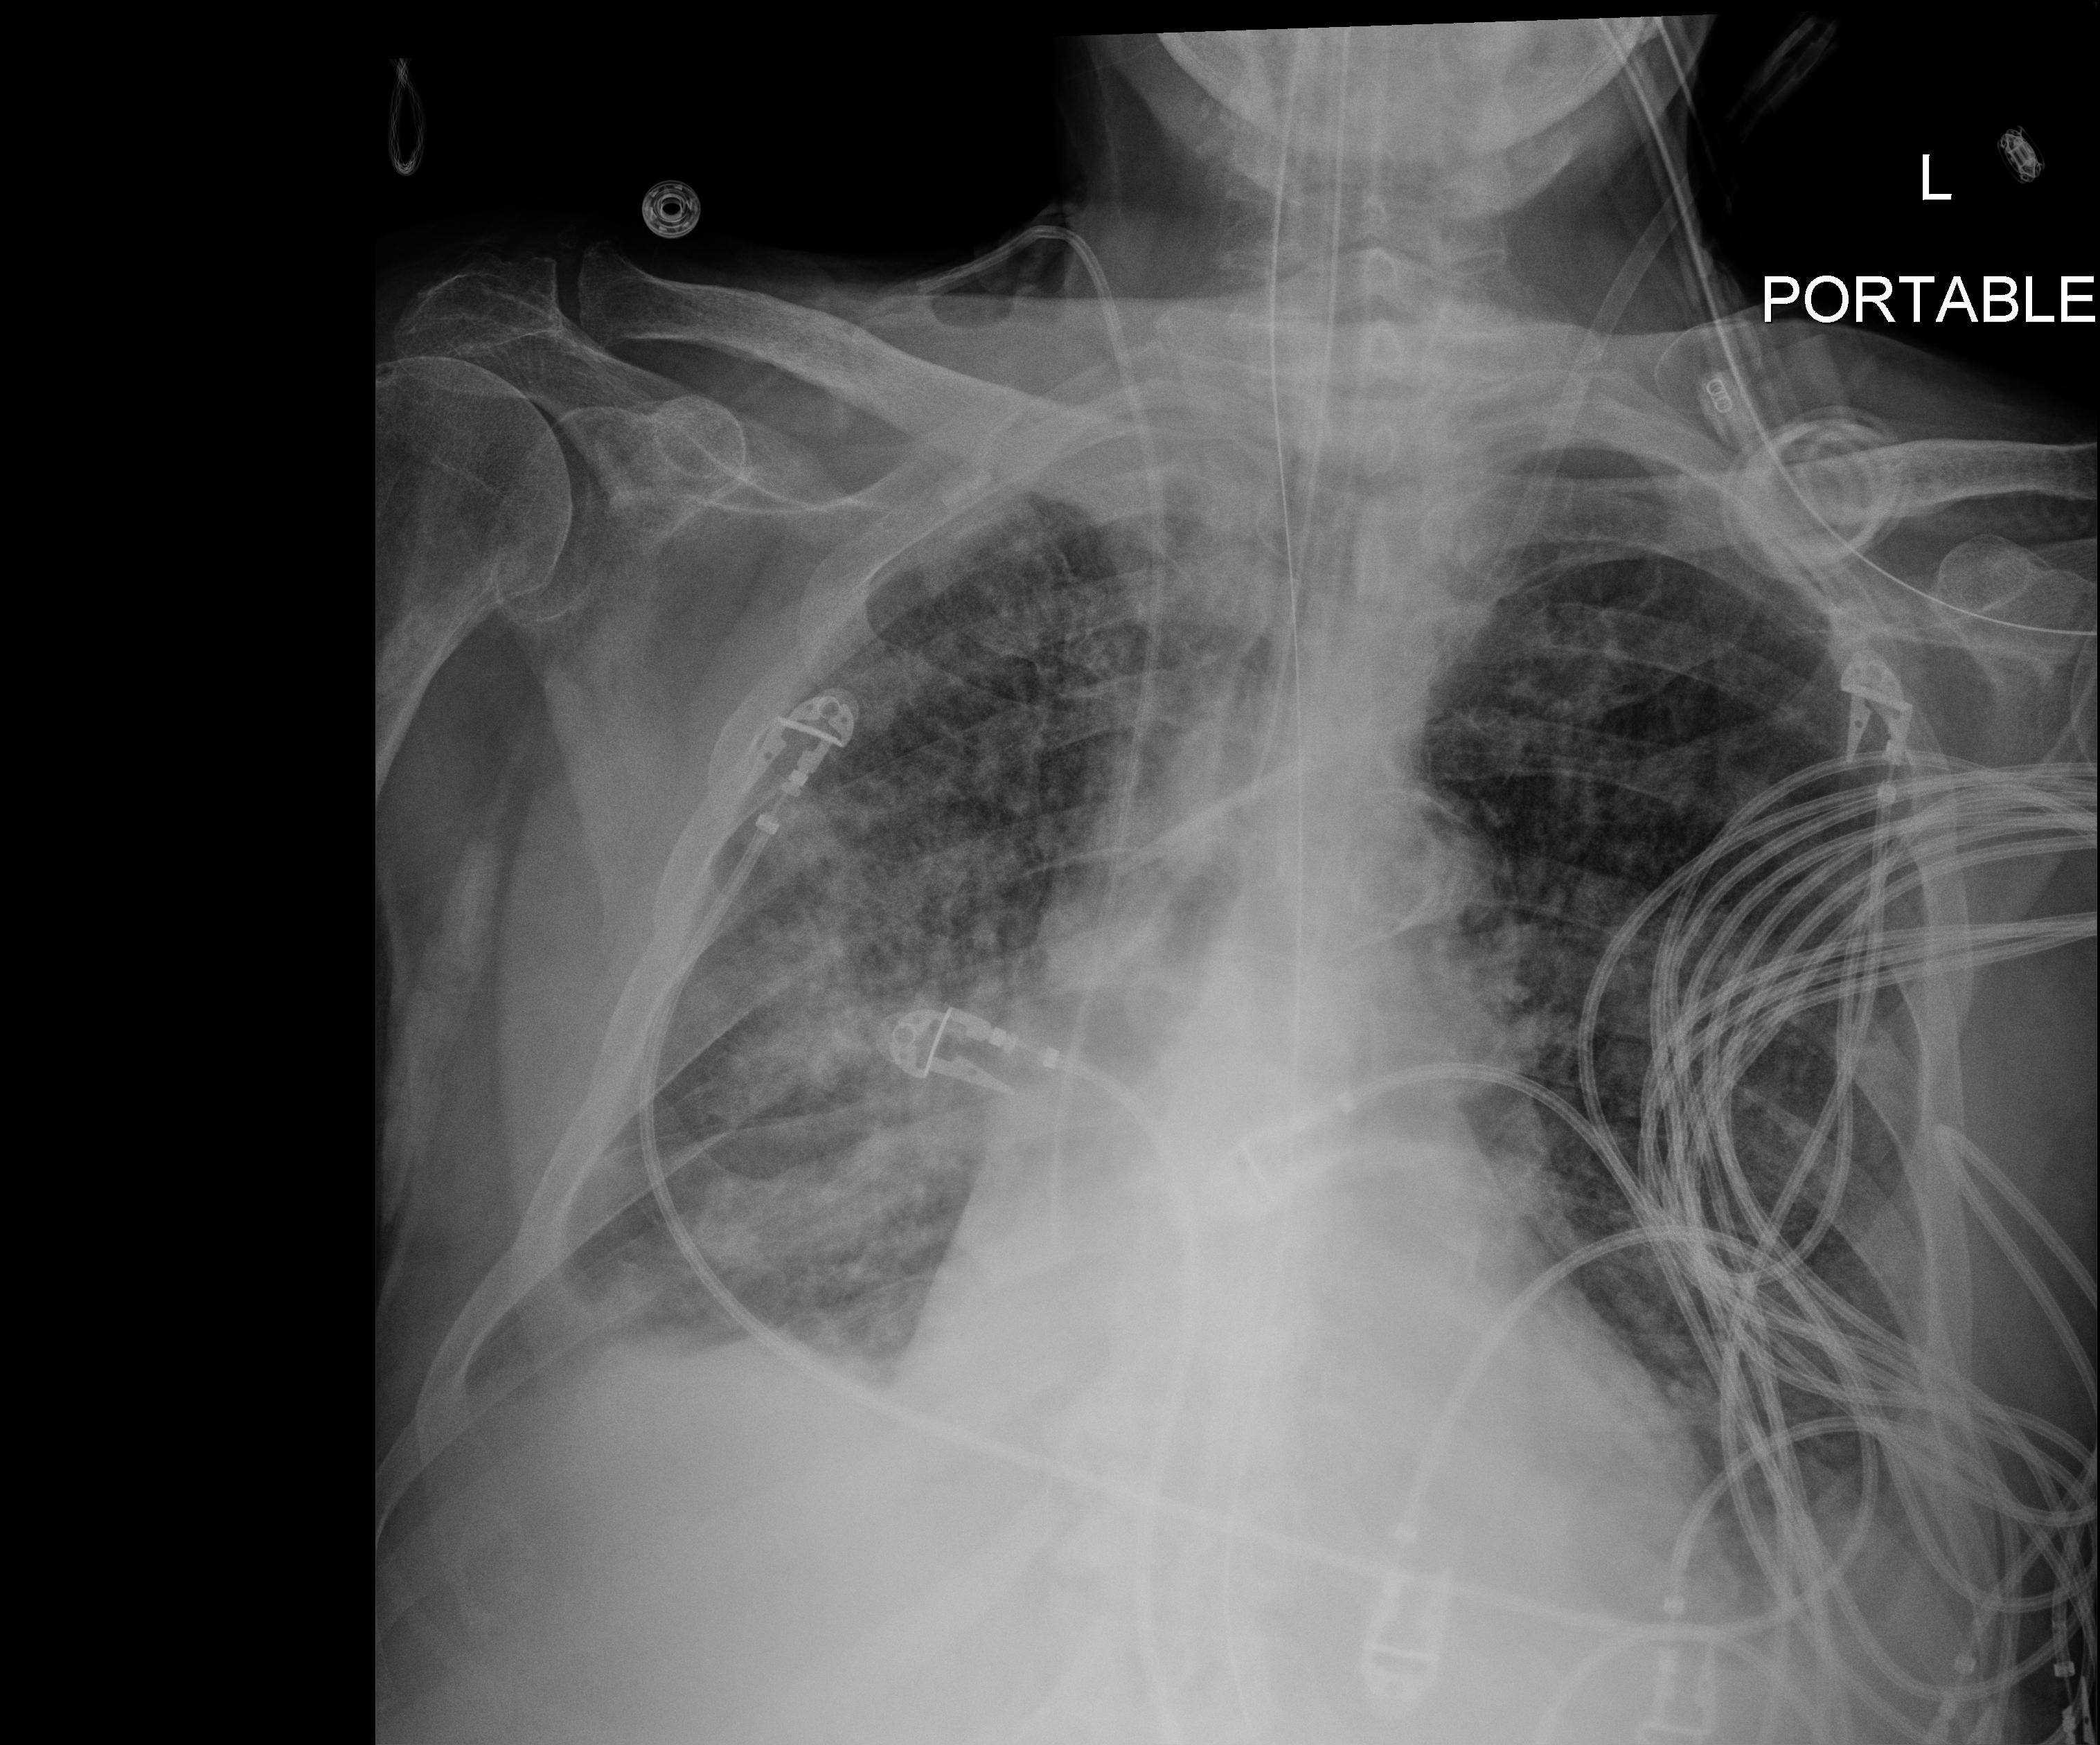
Chest X-ray (portable), anteroposterior (AP) projection. Male patient hospitalised with COVID-19, age 75–90 years.
From the hospital-stay record, not from the radiograph (when in the stay this image was taken is not recorded):
- mechanically ventilated during this hospital stay: yes